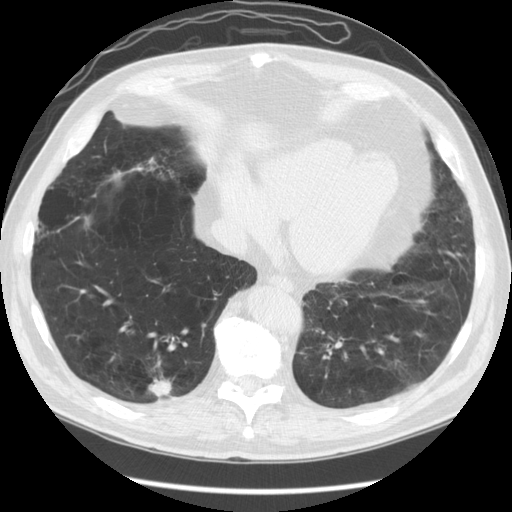
Low-dose screening chest CT, one axial slice; slice 43 of 141 in the series (ordered by position); lung window (W 1500 / L -600 HU); 2.5 mm slice thickness; 512 × 512 image matrix.
Annotated regions visible in this slice (manually delineated by an expert):
- lesion 1 (tumor, lower lobe of right lung): box from (x=148, y=375) to (x=172, y=396) px